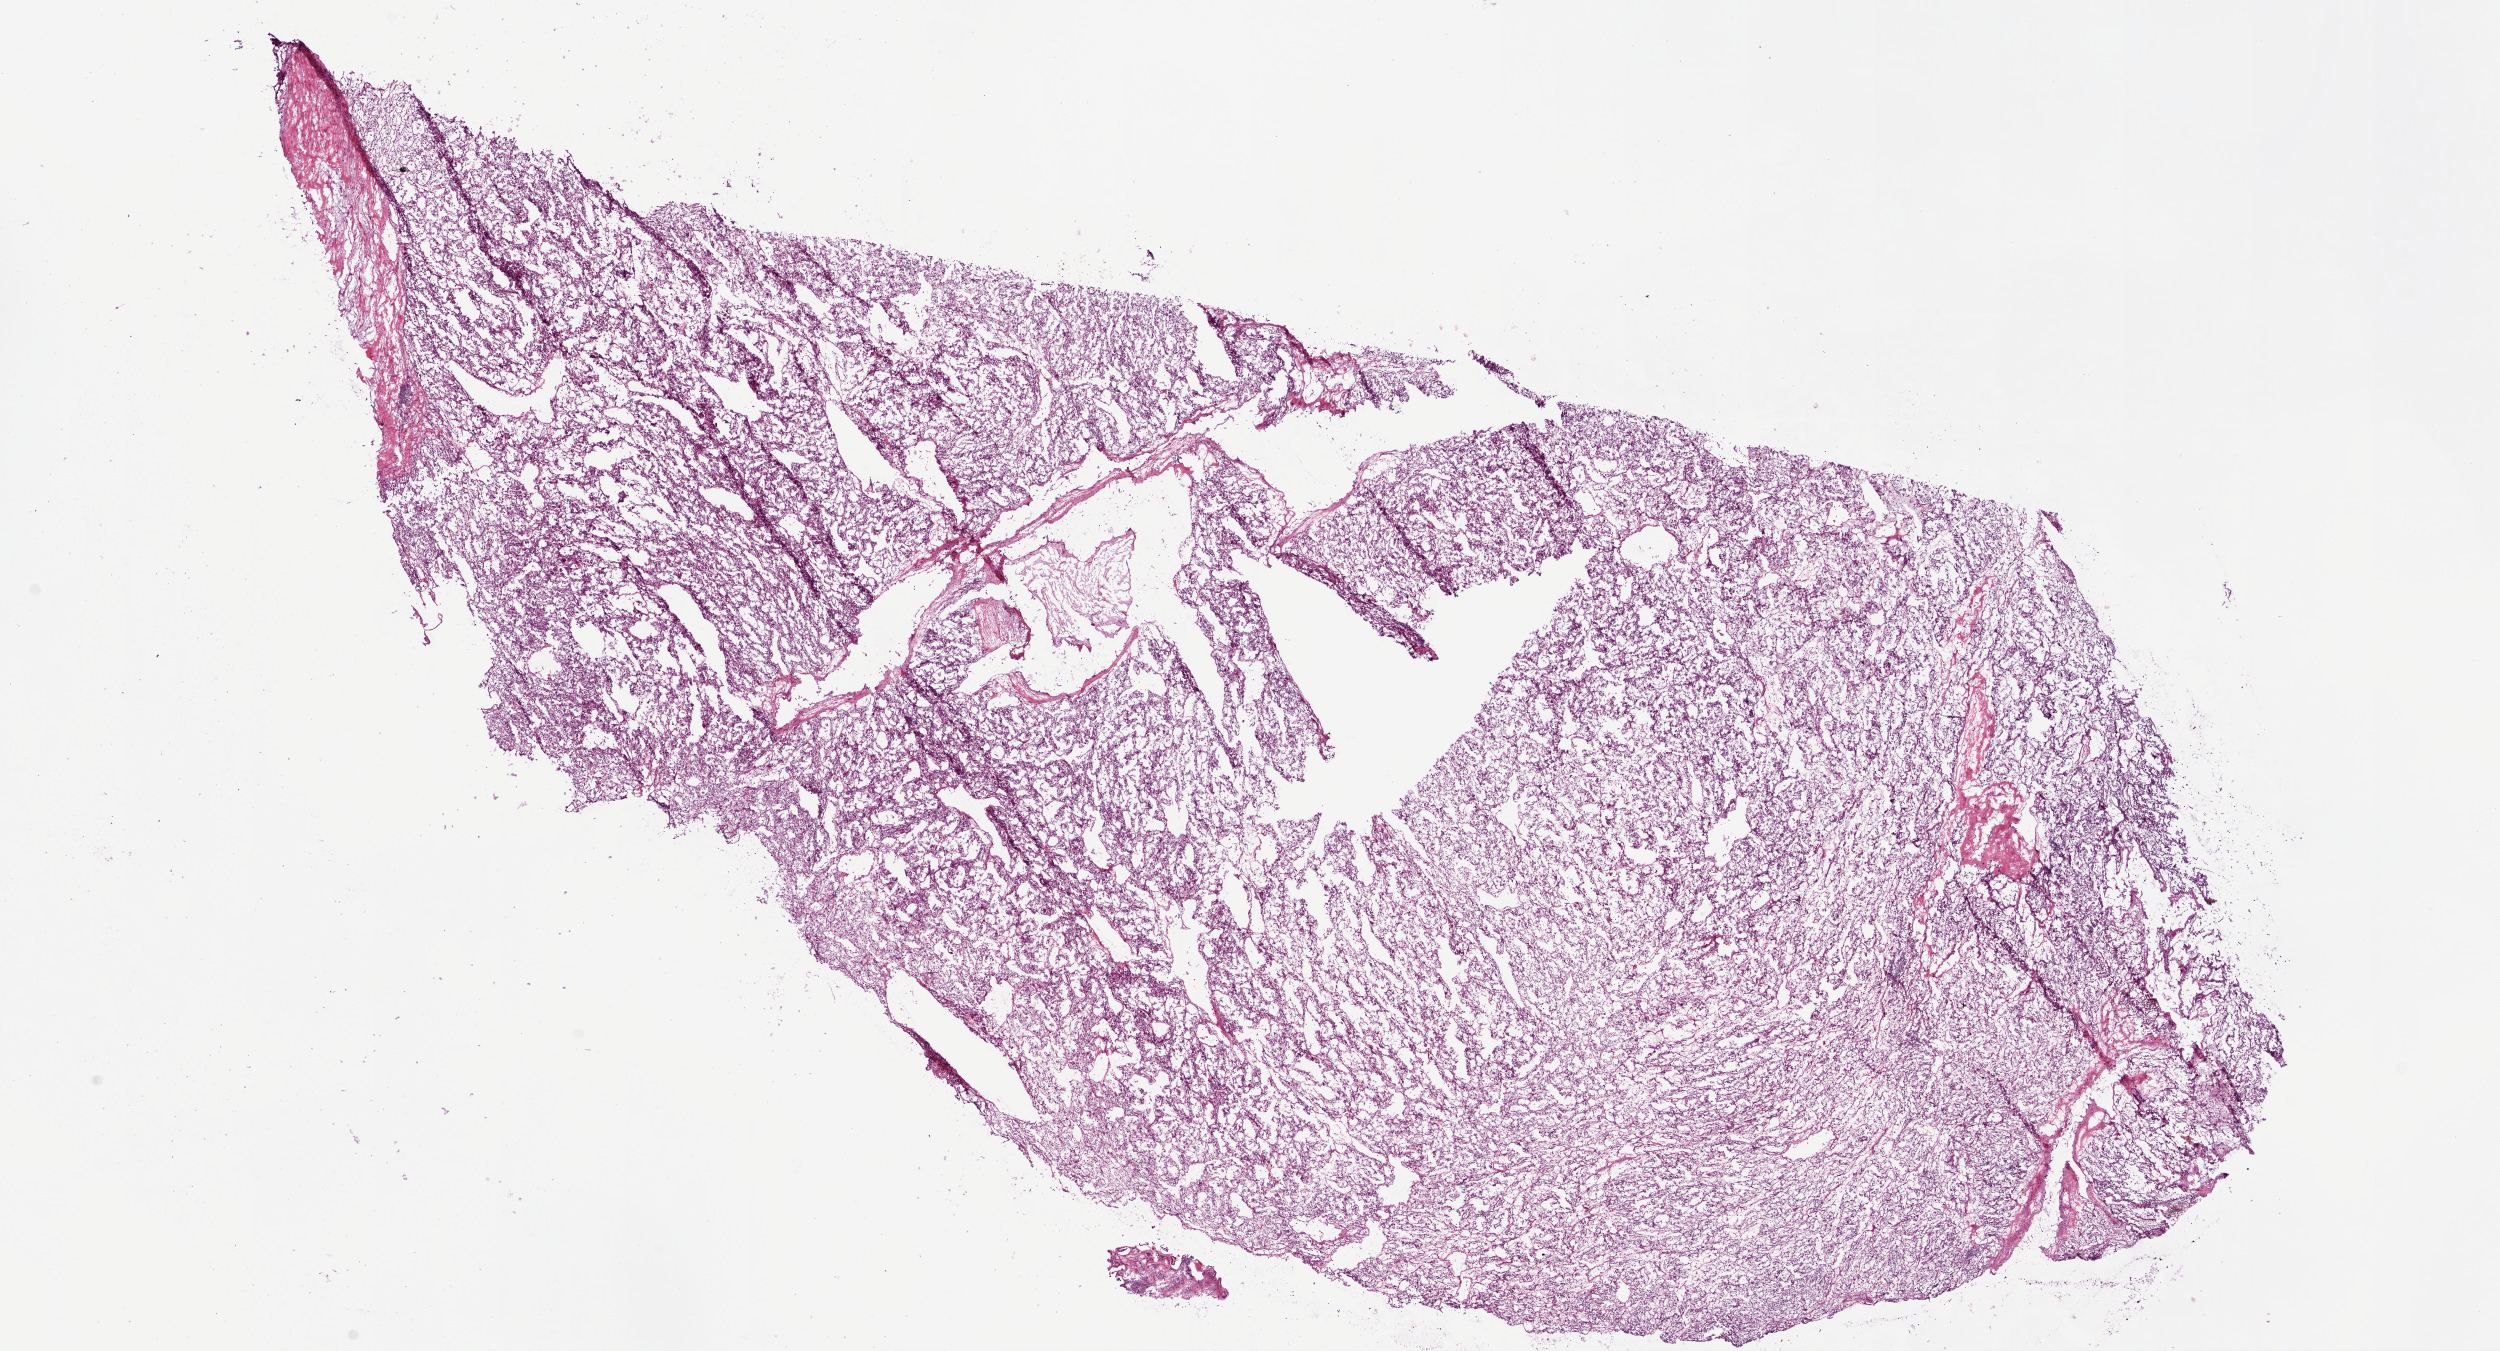
Whole-slide histology image, H&E — whole scanned area (about 20.1 x 10.8 mm) shown as a low-resolution overview; frozen section; sample: primary tumour, kidney. Male patient; age at initial diagnosis 73 years. Histologic grade: G3 (poorly differentiated). Slide review estimates, as recorded: tumour cells 90%, tumour nuclei 85%, normal cells 0%, stromal cells 10%, necrosis 0%.
Histologic diagnosis: Clear cell adenocarcinoma, NOS. Laterality: left. AJCC pathologic stage: I.